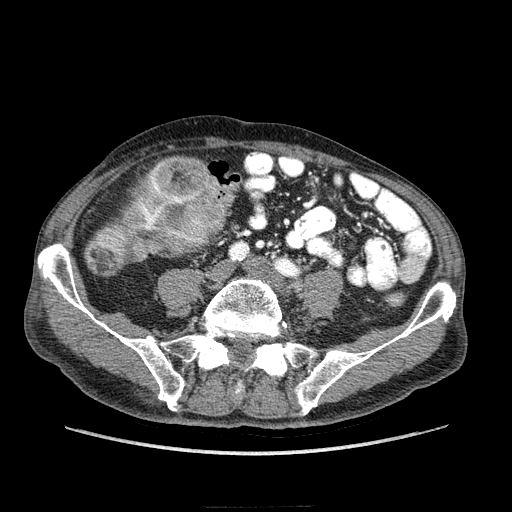
Contrast-enhanced abdominal CT (liver protocol), one axial slice. Slice 25 of 218 in the series (ordered by position). Reconstruction kernel STANDARD. 100 kVp. Soft-tissue window (W 400 / L 40 HU). 512 × 512 image matrix, field of view 380 × 380 mm. Case-level facts recorded for this patient, not image findings: diagnosis: hepatocellular carcinoma (patient treated with transarterial chemoembolisation; whether this scan precedes or follows treatment is not stated here); TNM stage (as recorded): Stage-IIIA; Child-Pugh class: A; tumour differentiation: well differentiated; tumour nodularity: multinodular.
Outlined on this slice (semi-automatically segmented with operator editing):
- mass: bounding box <83,156,238,277> (left, top, right, bottom; pixels)